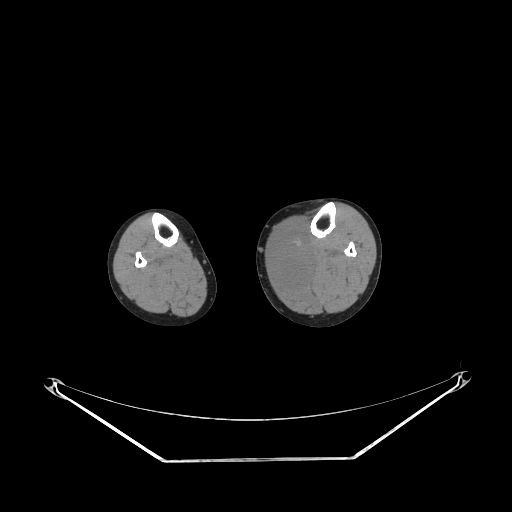
CT of an extremity soft-tissue mass (from a PET/CT study), one axial slice; slice 135 of 223 in the series (ordered by position); reconstruction kernel STANDARD; 140 kVp; soft-tissue window (W 400 / L 40 HU); 512 × 512 image matrix. Female patient. From the clinical record (not read from this slice): histological type: extraskeletal high grade osteogenic sarcoma; grade: high; site of the primary tumour: left calf.
Annotated regions visible in this slice (expert contour drawn on MRI and transferred to this co-registered scan by the dataset authors):
- gross tumour volume (mass): bounding box [x1, y1, x2, y2] px = [272, 231, 312, 286]